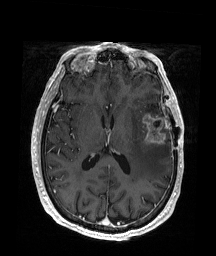
Brain MRI from a brain-tumour surgery series, one axial slice. Position 88 of 176 along the scan axis. T1-weighted post-contrast. 216 × 256 image matrix. From the clinical record (not read from this slice): histopathology: Glioblastoma; WHO grade: 4; IDH mutation: no; tumour location: Left Frontal.
Outlined on this slice (expert manual segmentation):
- tumour: bounding box <141,113,167,146> (left, top, right, bottom; pixels)